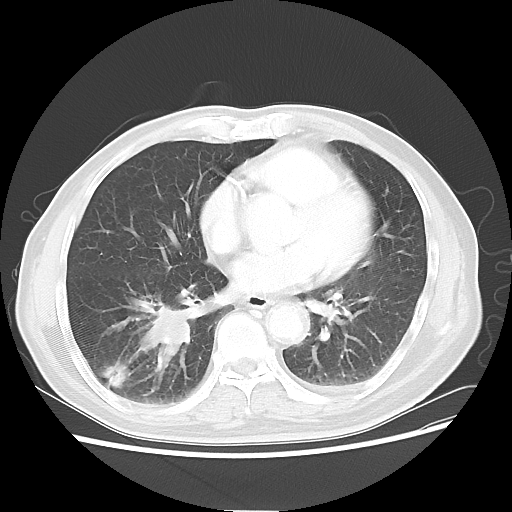
Chest CT, one axial slice; lung window (W 1500 / L -600 HU); 5 mm slice thickness; 512 × 512 image matrix. Male patient, age 74 years. Case-level facts recorded for this patient, not image findings: clinical TNM (as recorded): T1c N1 M1.
Outlined on this slice (bounding box drawn by a radiologist):
- lung tumour (recorded histology: adenocarcinoma): bounding box (x1, y1, x2, y2) in pixels: (119, 291, 200, 362)